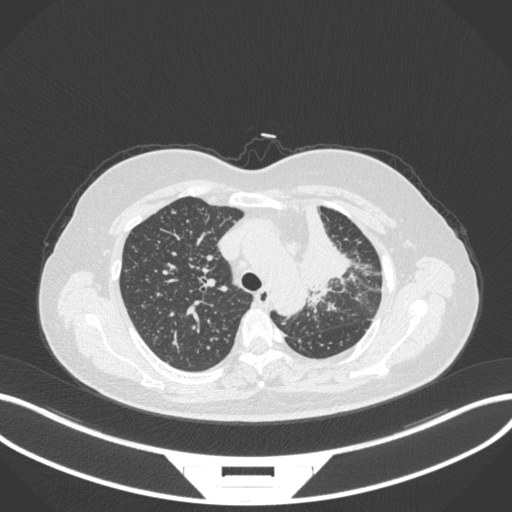
Chest CT, one axial slice. Reconstruction kernel B31f. Lung window (W 1500 / L -600 HU). 512 × 512 image matrix, field of view 400 × 400 mm. Female patient, age 49 years. From the clinical record (not read from this slice): clinical TNM (as recorded): T1c N0 M1.
Annotated regions visible in this slice (bounding box drawn by a radiologist):
- lung tumour (recorded histology: adenocarcinoma): box from (x=299, y=204) to (x=355, y=293) px